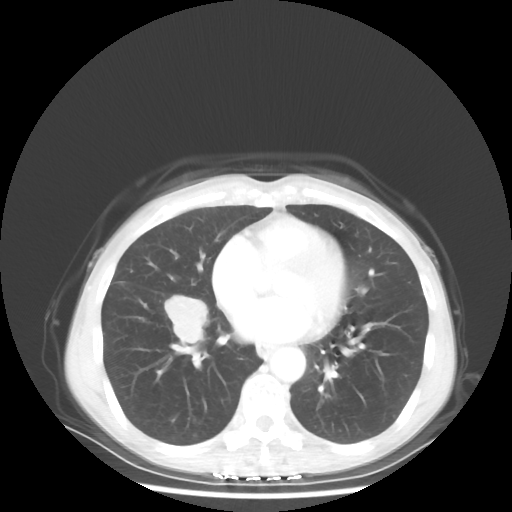
Chest CT, one axial slice; position 22 of 56 along the scan axis; reconstruction kernel STANDARD; 80 kVp; lung window (W 1500 / L -600 HU); 512 × 512 image matrix, field of view 360 × 360 mm. Female patient, age 57 years. From the clinical record (not read from this slice): clinical TNM (as recorded): T1c N3 M1a.
Annotated regions visible in this slice (rectangle marked by the reading radiologist):
- lung tumour (recorded histology: adenocarcinoma): box from (x=163, y=292) to (x=210, y=345) px